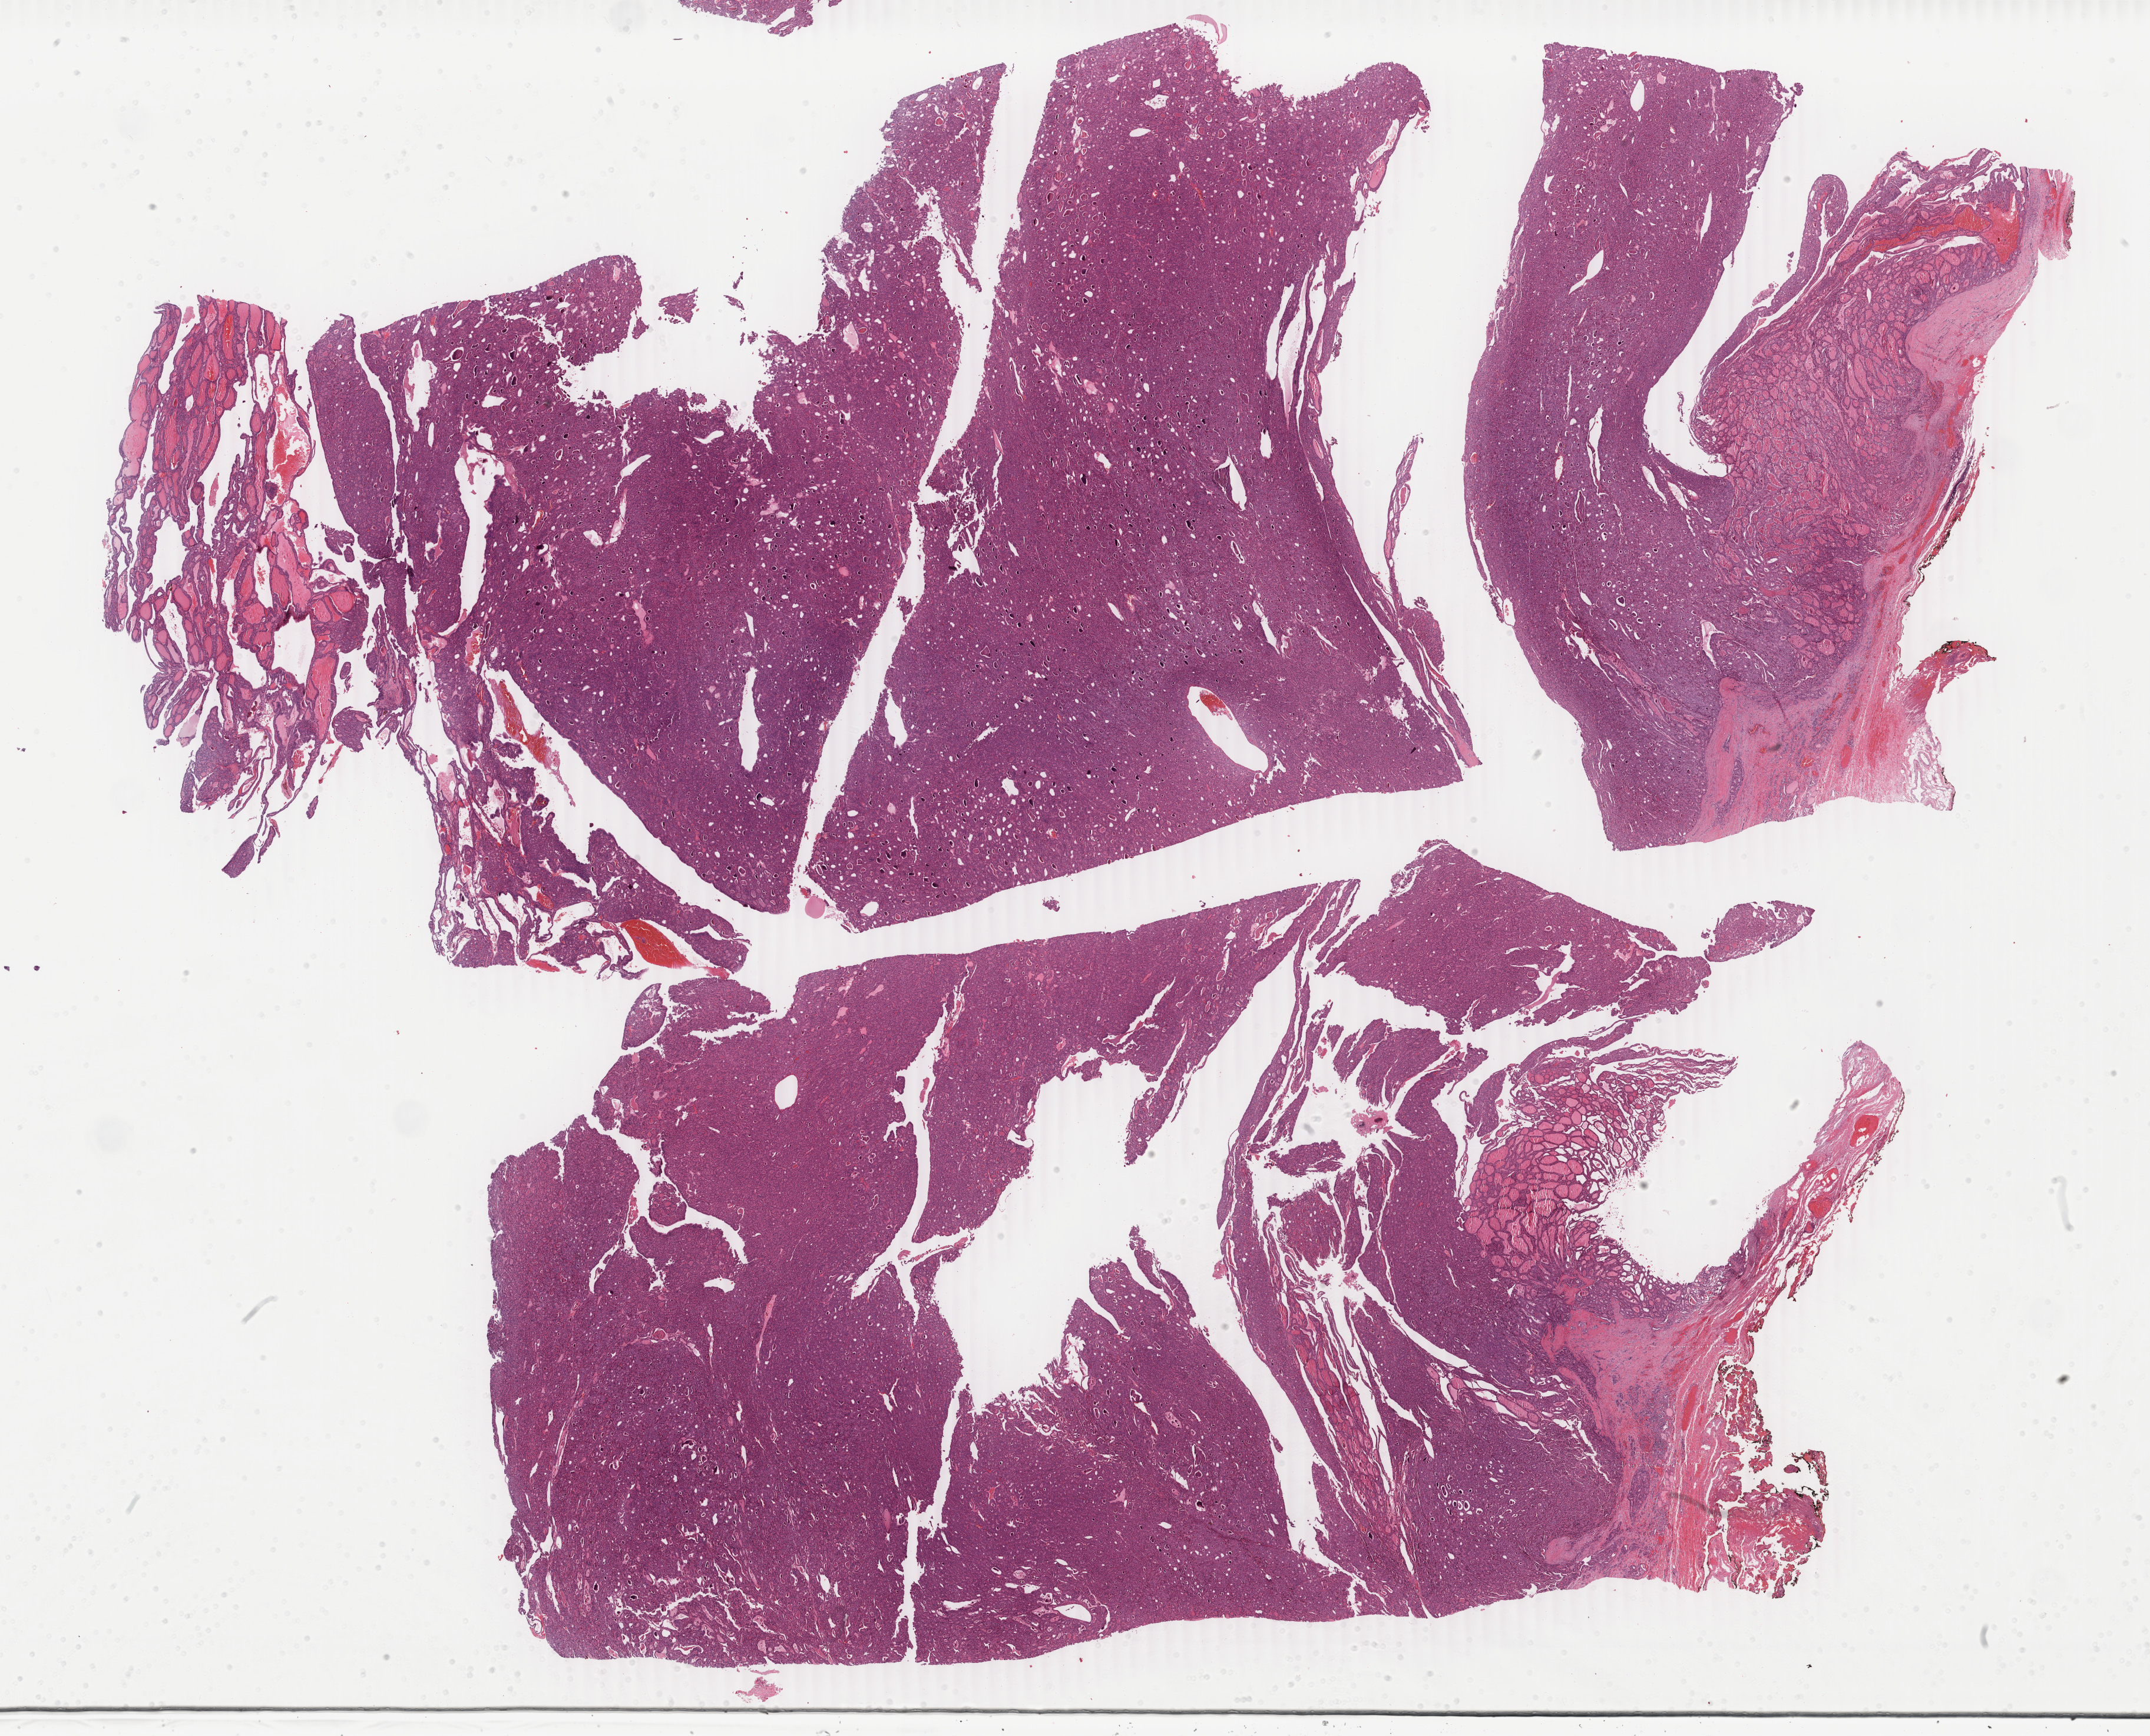
Digitized Hematoxylin and eosin (H&E) stained tissue section (whole slide), shown as a low-resolution overview of the whole scanned area (about 29.0 x 23.4 mm), formalin-fixed paraffin-embedded (FFPE) diagnostic section, primary tumour sample from the thyroid. Female patient; age at initial diagnosis 19 years.
Histologic diagnosis: Papillary adenocarcinoma, NOS (thyroid gland). Laterality: bilateral. AJCC pathologic stage: I (6th edition).